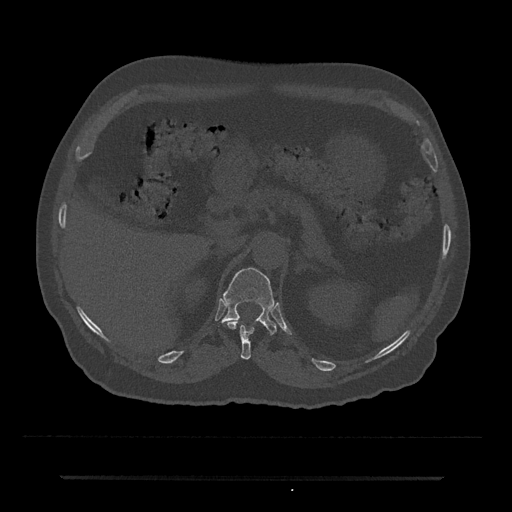
CT including the spine, one axial slice. Position 146 of 797 along the scan axis. Reconstruction kernel Br40s/3. 120 kVp. Bone window (W 1800 / L 400 HU). 0.5 mm slice thickness. 512 × 512 image matrix, field of view 437 × 437 mm. Patient: male, 69 years. From the clinical record (not read from this slice): primary cancer: prostate.
Annotated regions visible in this slice (semi-automatic segmentation, software-assisted and operator-edited):
- T11 vertebra: bounding box (x1, y1, x2, y2) in pixels: (227, 321, 255, 360)
- T12 vertebra: (218, 267, 276, 334)